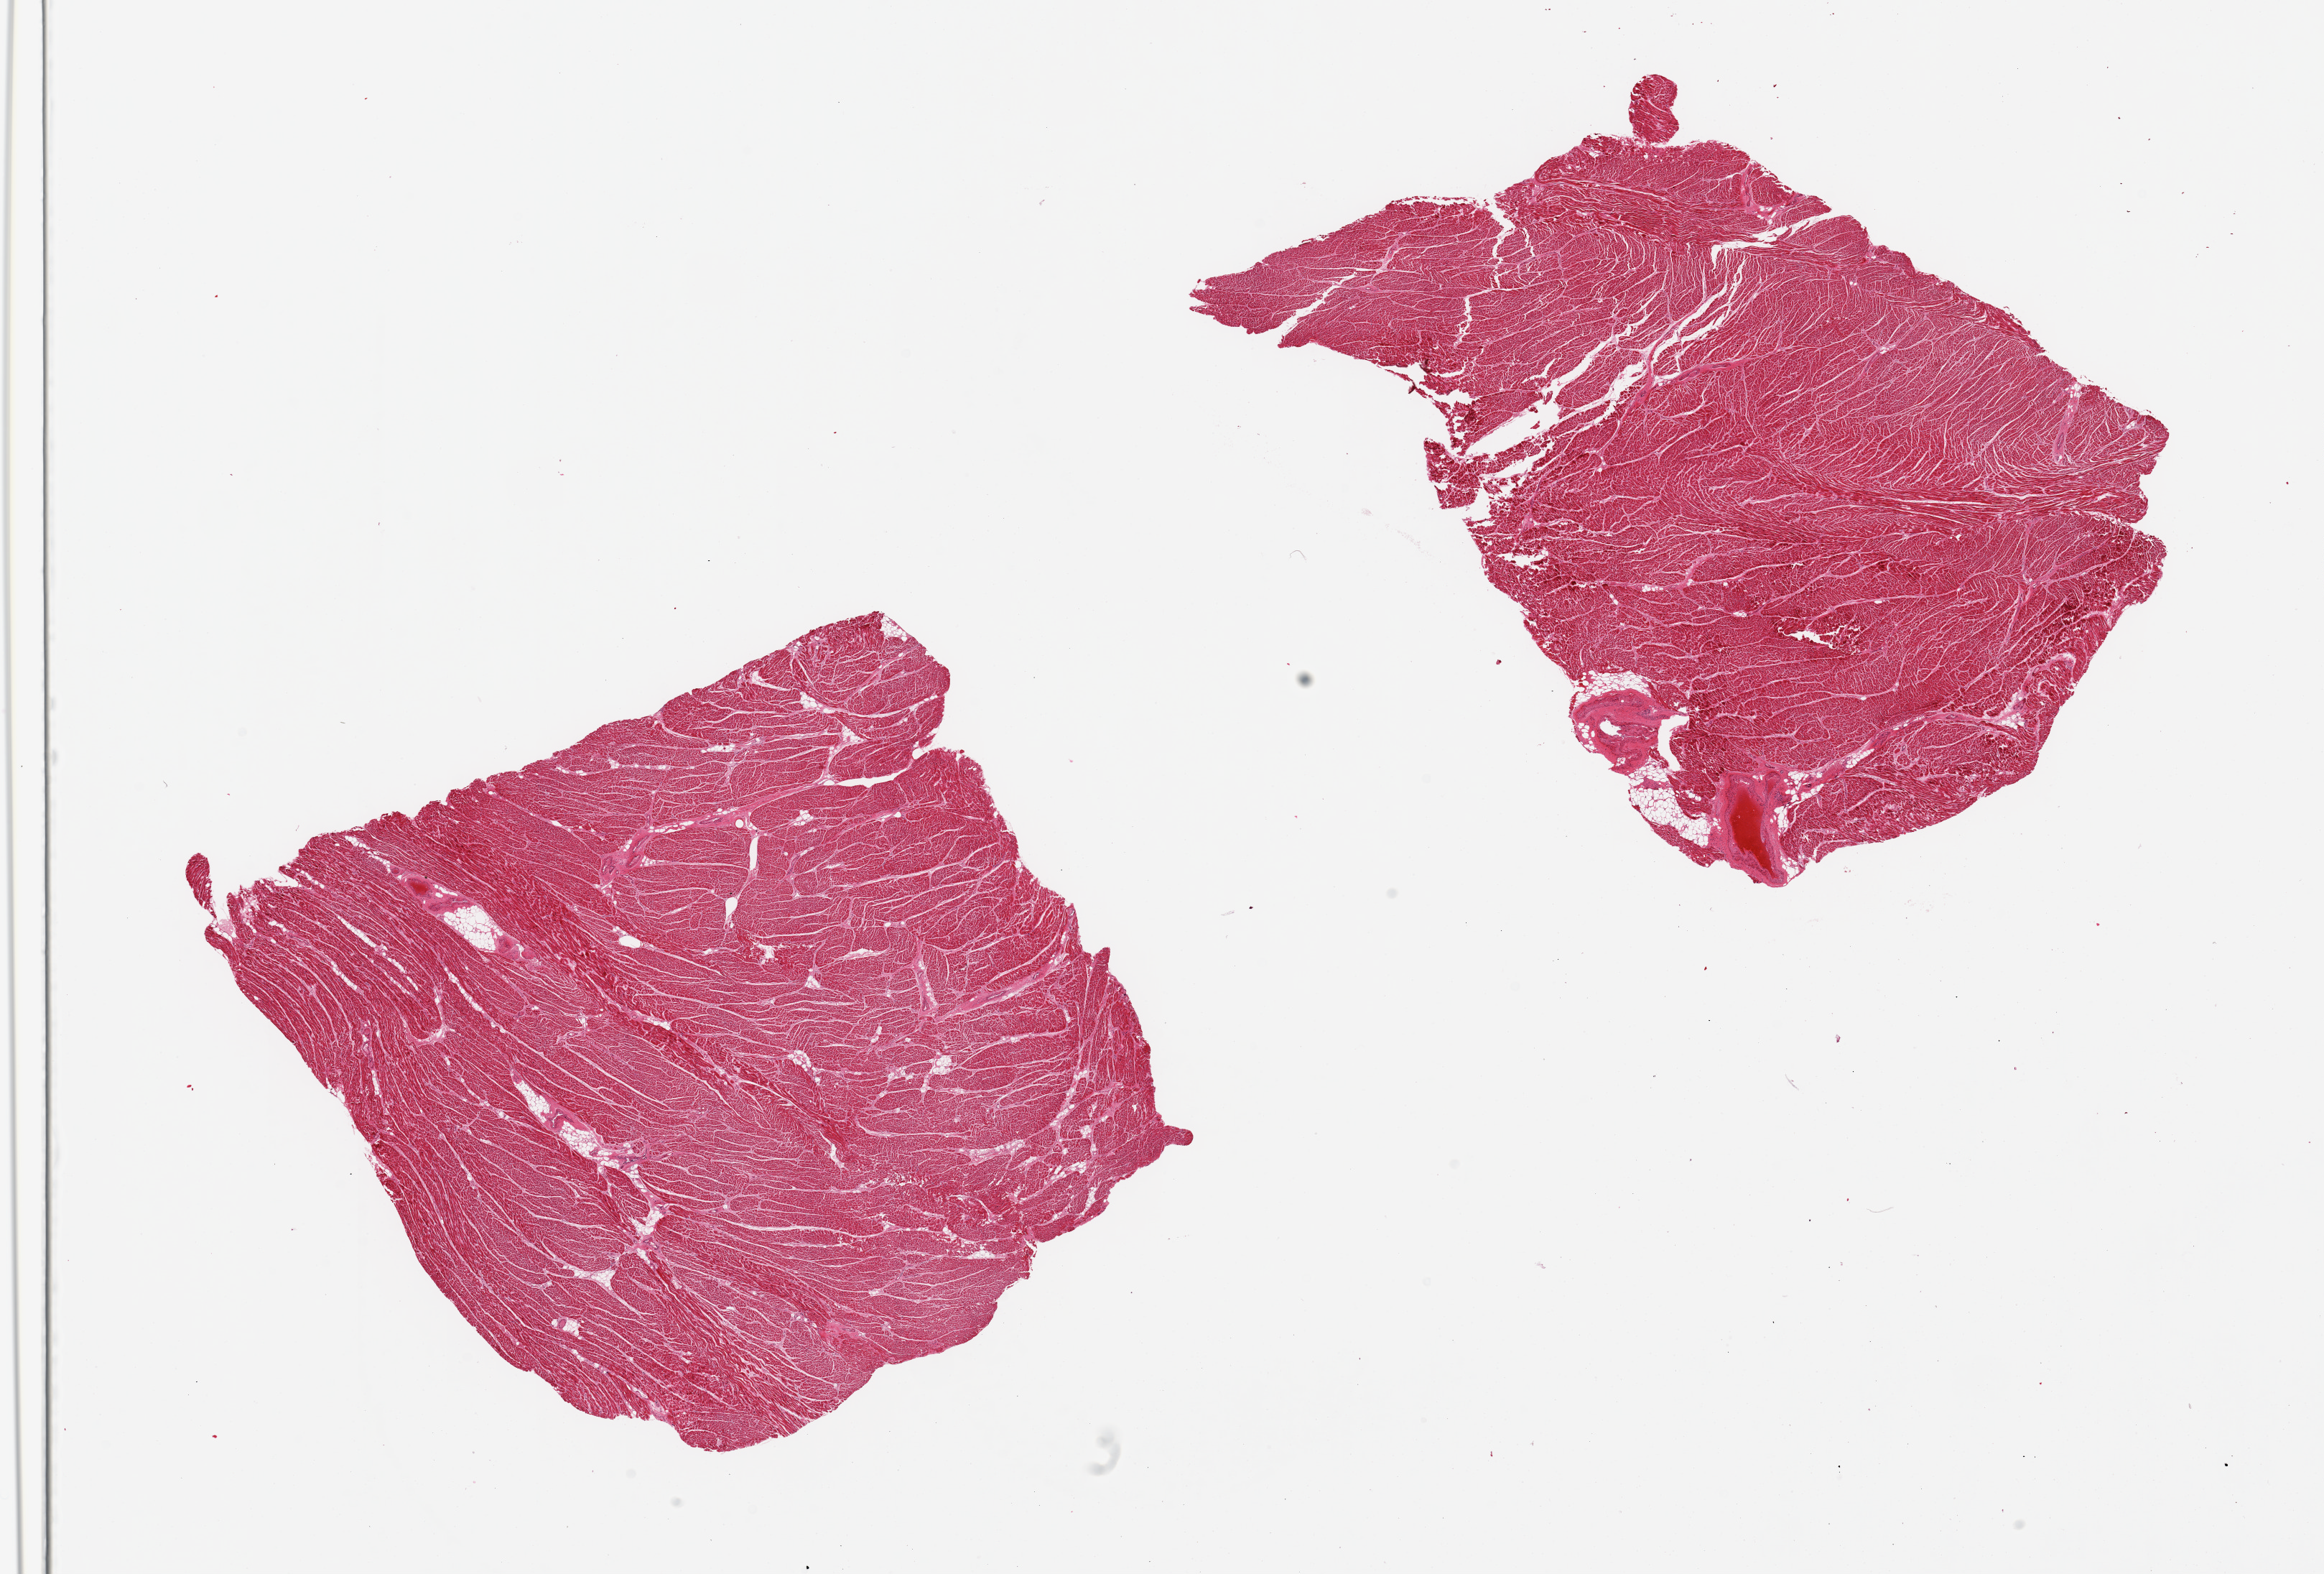
H&E whole-slide image, shown as a low-resolution overview of the whole scanned area (about 25.6 x 17.3 mm, slide scanned at 20x); PAXgene-fixed paraffin-embedded (PFPE) section; sampled site (target tissue): heart; donor tissue sample. Male donor.
Reviewer comment on this tissue sample: 2 pieces.